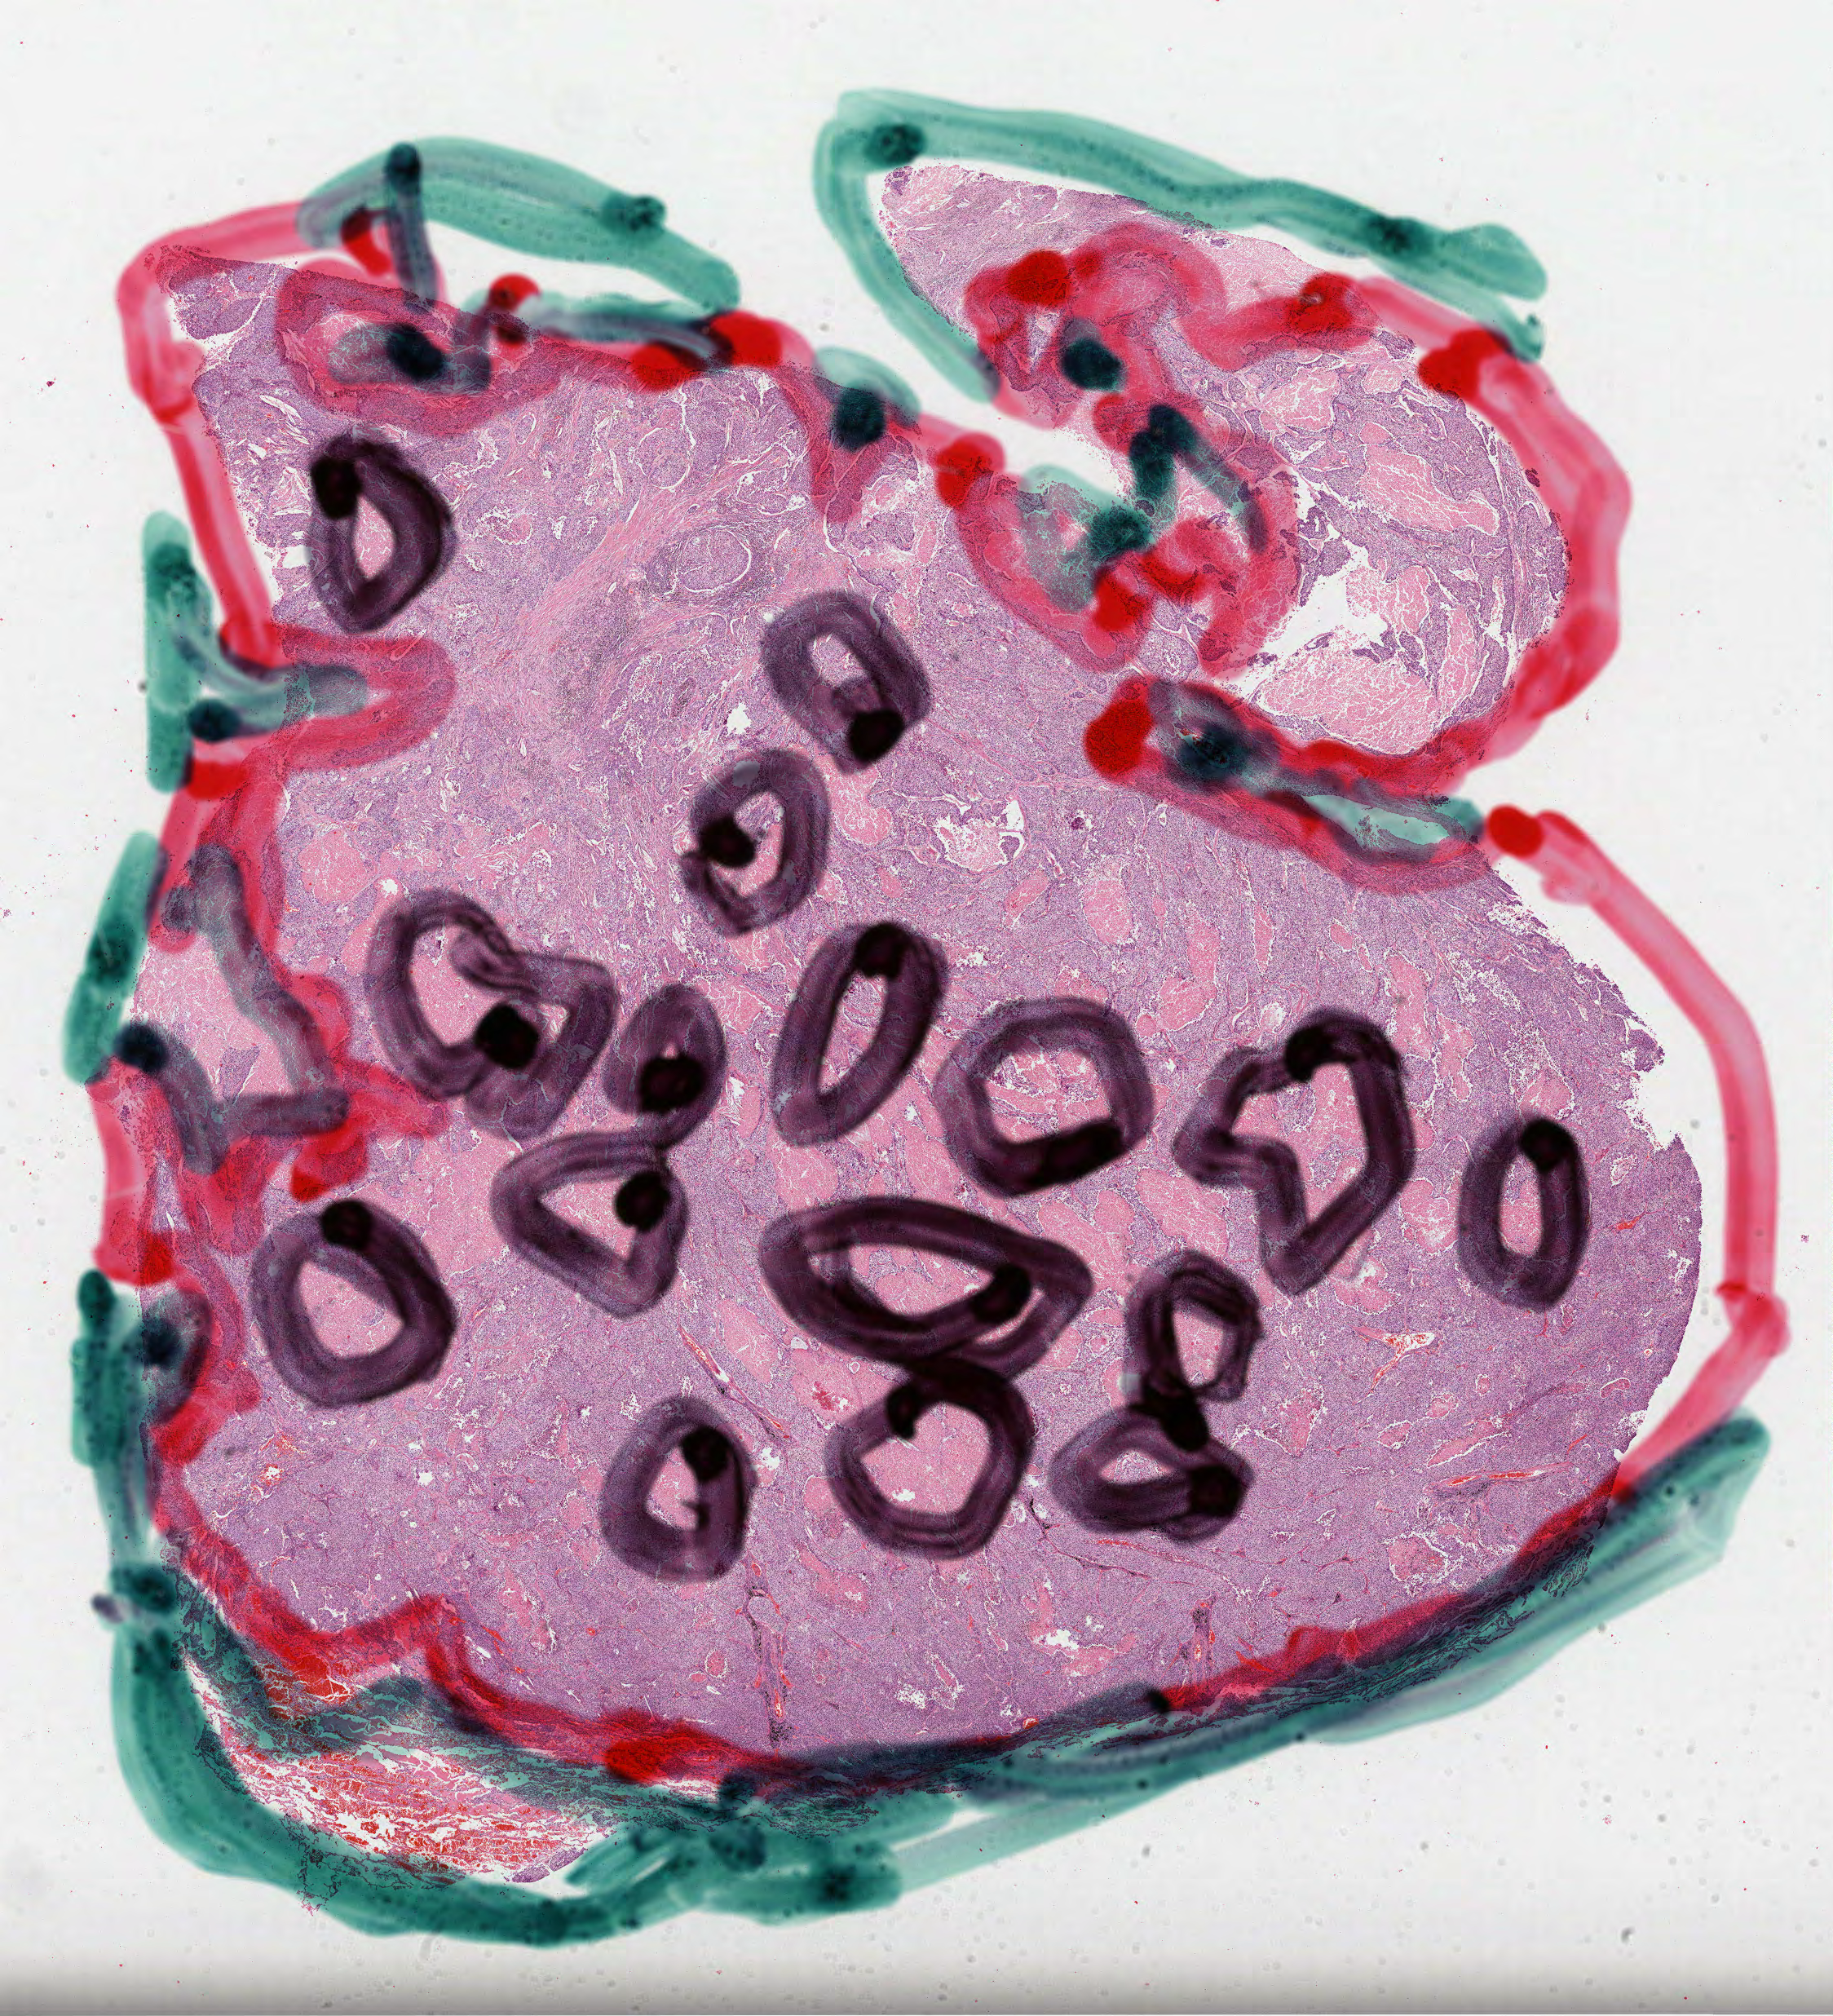
Digitized H&E-stained tissue section (whole slide), whole scanned area (about 18.1 x 19.9 mm, slide scanned at 40x) shown as a low-resolution overview, FFPE section, sample: primary tumour, lung. Male, age 71 years at initial diagnosis.
- laterality: left
- histologic diagnosis: Squamous cell carcinoma, NOS (upper lobe, lung)
- TNM: T2 N0 M0
- AJCC pathologic stage: IB